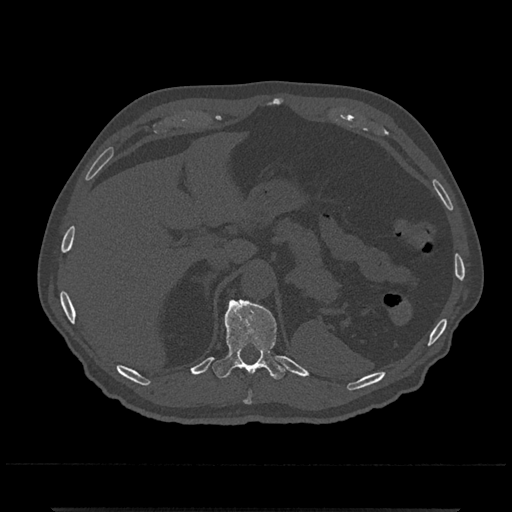
CT including the spine, one axial slice. Bone window (W 1800 / L 400 HU). 0.5 mm slice thickness. 512 × 512 image matrix, field of view 393 × 393 mm. Patient: male, 67 years. From the clinical record (not read from this slice): primary cancer: prostate.
Outlined on this slice (semi-automatic segmentation, software-assisted and operator-edited):
- T10 vertebra: bounding box (x1, y1, x2, y2) in pixels: (244, 391, 252, 404)
- T11 vertebra: (212, 299, 286, 380)